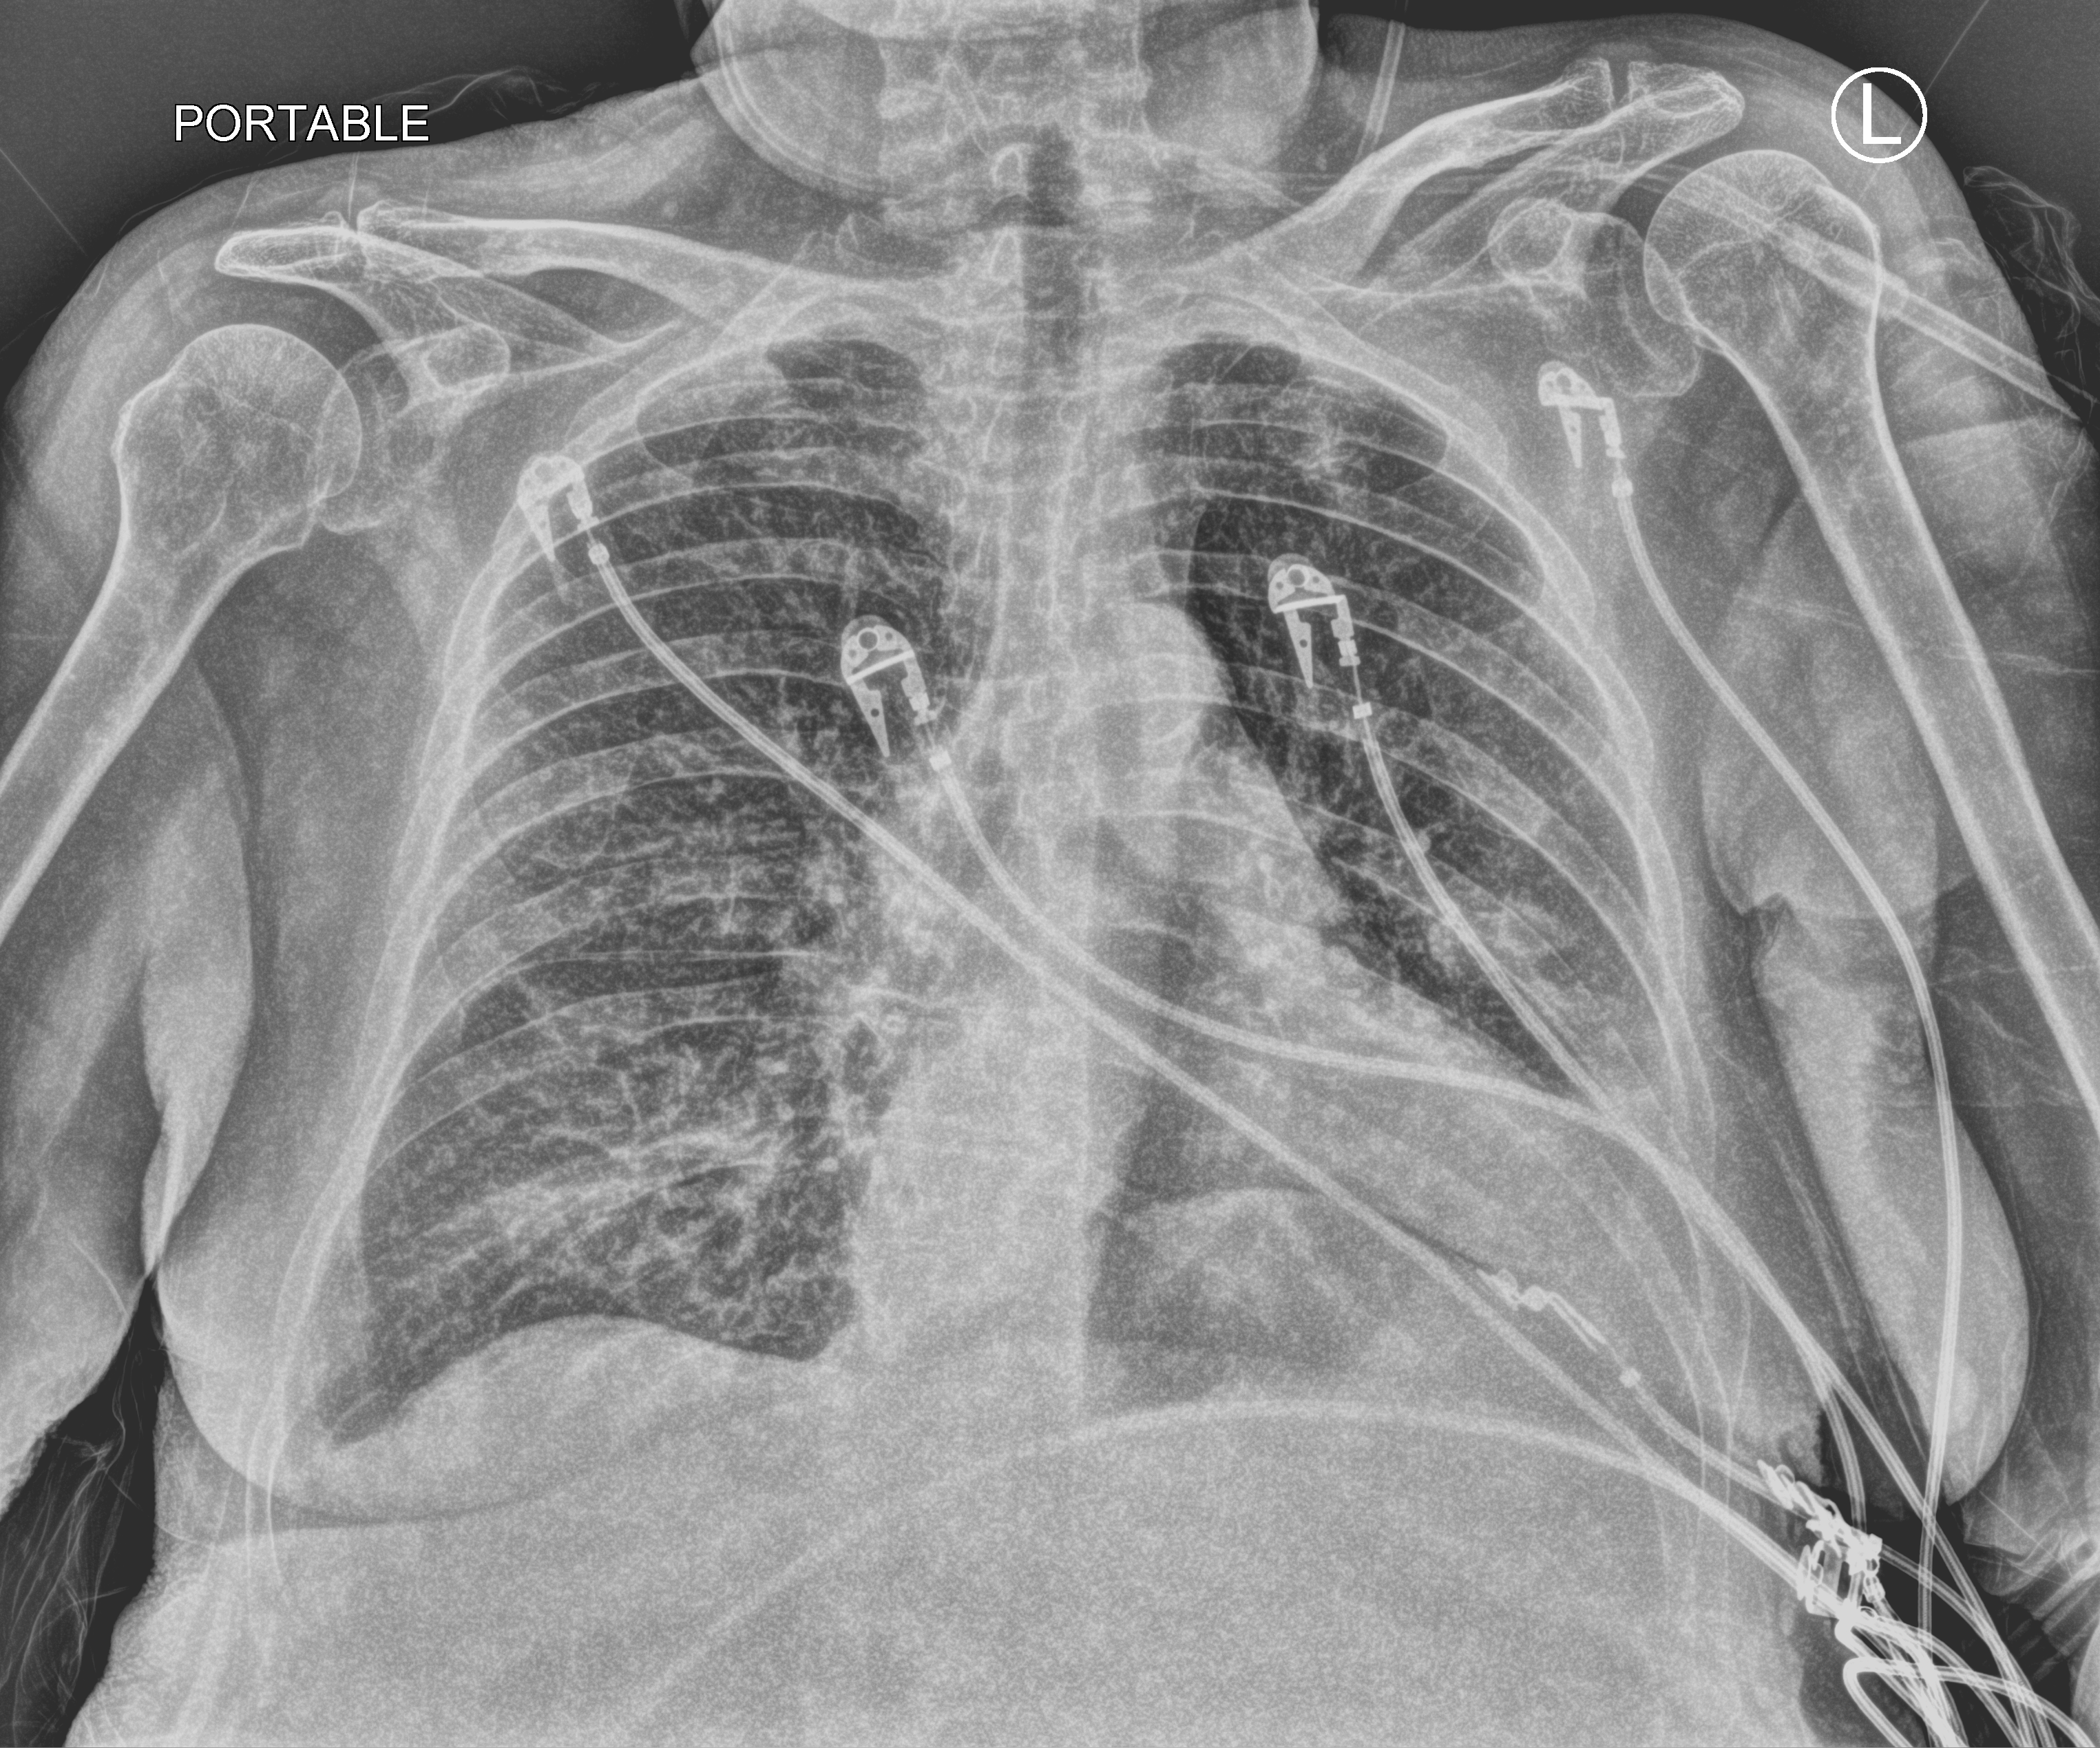
Portable chest radiograph; anteroposterior (AP) projection. Patient hospitalised with COVID-19; female, aged 75–90 years.
Hospital-stay facts (about this admission, not read from this image; timing relative to this image not recorded): length of hospital stay: 6 days; mechanically ventilated during this hospital stay: no; admitted to intensive care during this hospital stay: no.